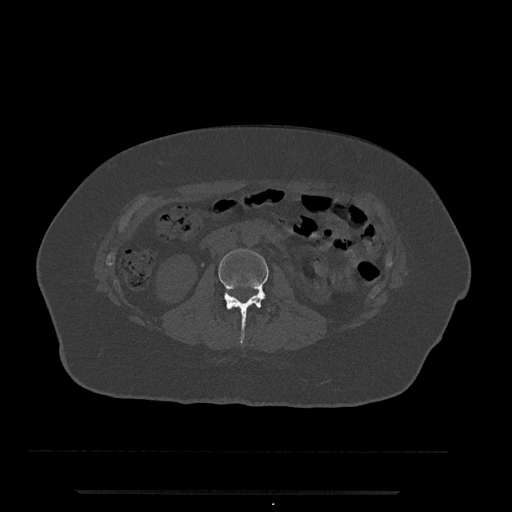
CT including the spine, one axial slice; position 32 of 797 along the scan axis; reconstruction kernel Br40s/3; 120 kVp; bone window (W 1800 / L 400 HU); 0.5 mm slice thickness; 512 × 512 image matrix, field of view 440 × 440 mm. Female patient, age 51 years. From the clinical record (not read from this slice): primary cancer: neuro; vertebrae with lytic lesions (as recorded): T8.
Outlined on this slice (semi-automatically segmented with operator editing):
- L2 vertebra: bounding box <219,249,269,340> (left, top, right, bottom; pixels)